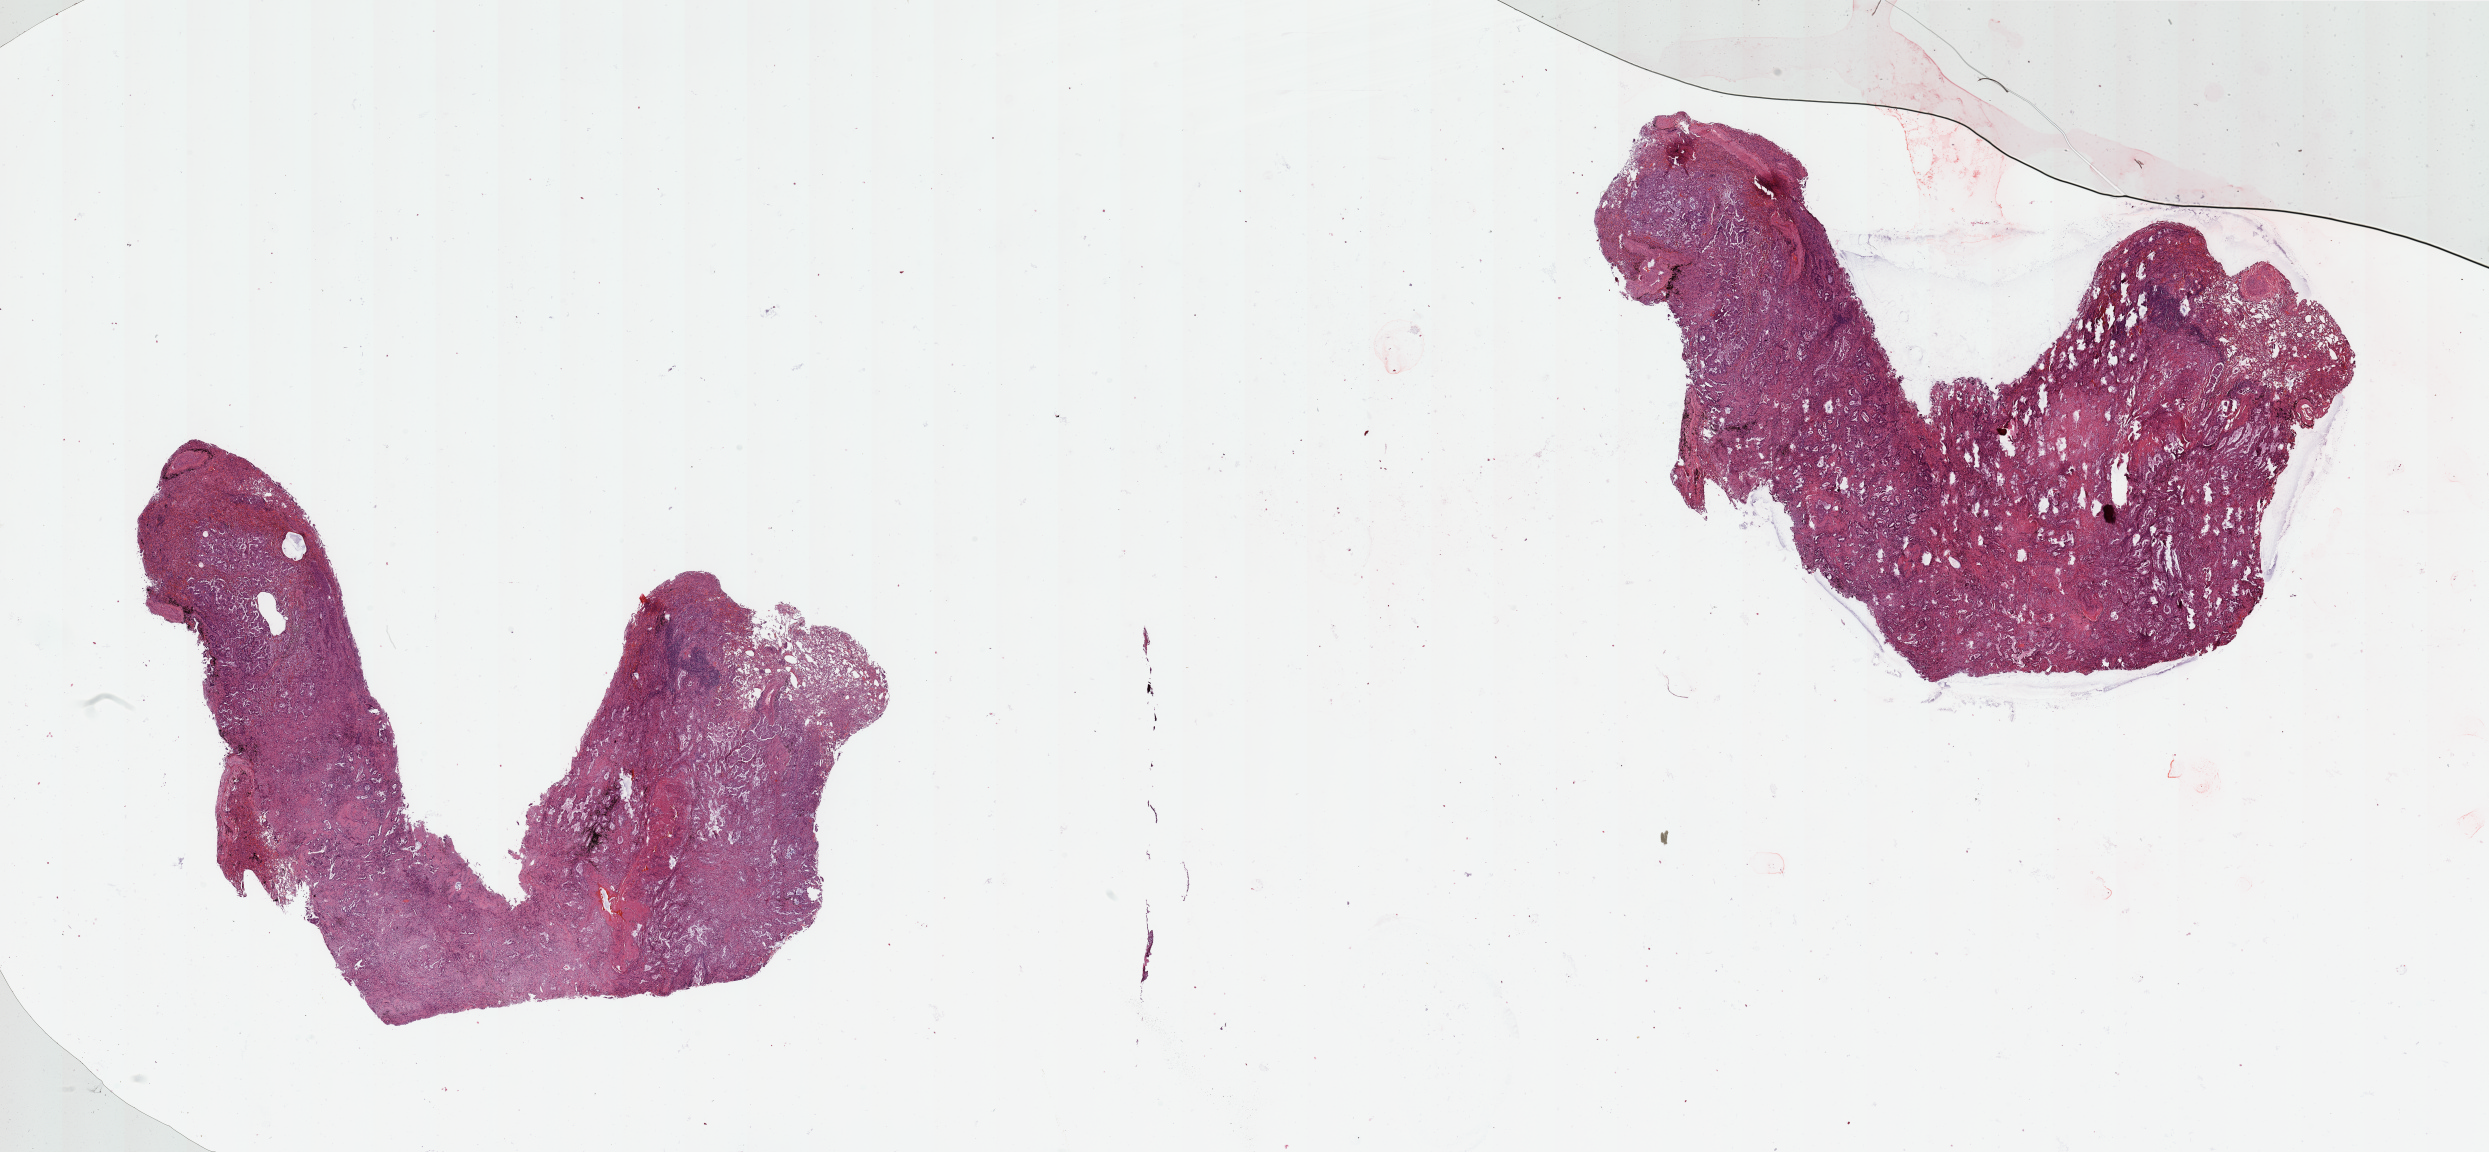
Whole-slide histology image, Hematoxylin and eosin (H&E) stained — shown as a low-resolution overview of the whole scanned area (about 39.4 x 18.2 mm, acquisition: 20x scan), tumour tissue sample, lung. Female, 70 y/o. Histologic grade: G1 (well differentiated).
AJCC pathologic stage: IIIA. Diagnosis: Adenocarcinoma, NOS.